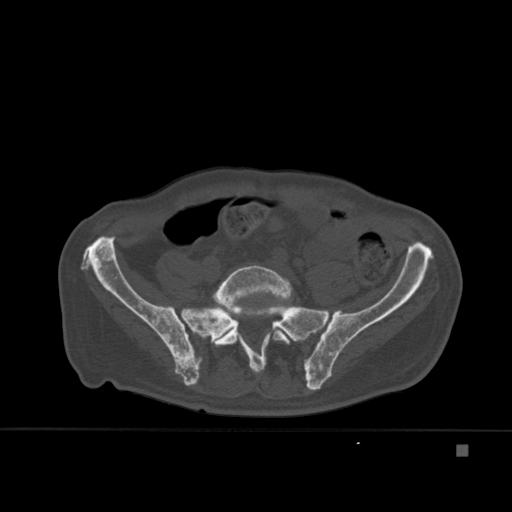
CT including the spine, one axial slice; slice 95 of 451 in the series (ordered by position); bone window (W 1800 / L 400 HU); 1.5 mm slice thickness; 512 × 512 image matrix. Patient: male, 75 years. From the clinical record (not read from this slice): primary cancer: prostate.
Annotated regions visible in this slice (semi-automatically segmented with operator editing):
- L5 vertebra: bounding box [x1, y1, x2, y2] px = [211, 265, 293, 367]